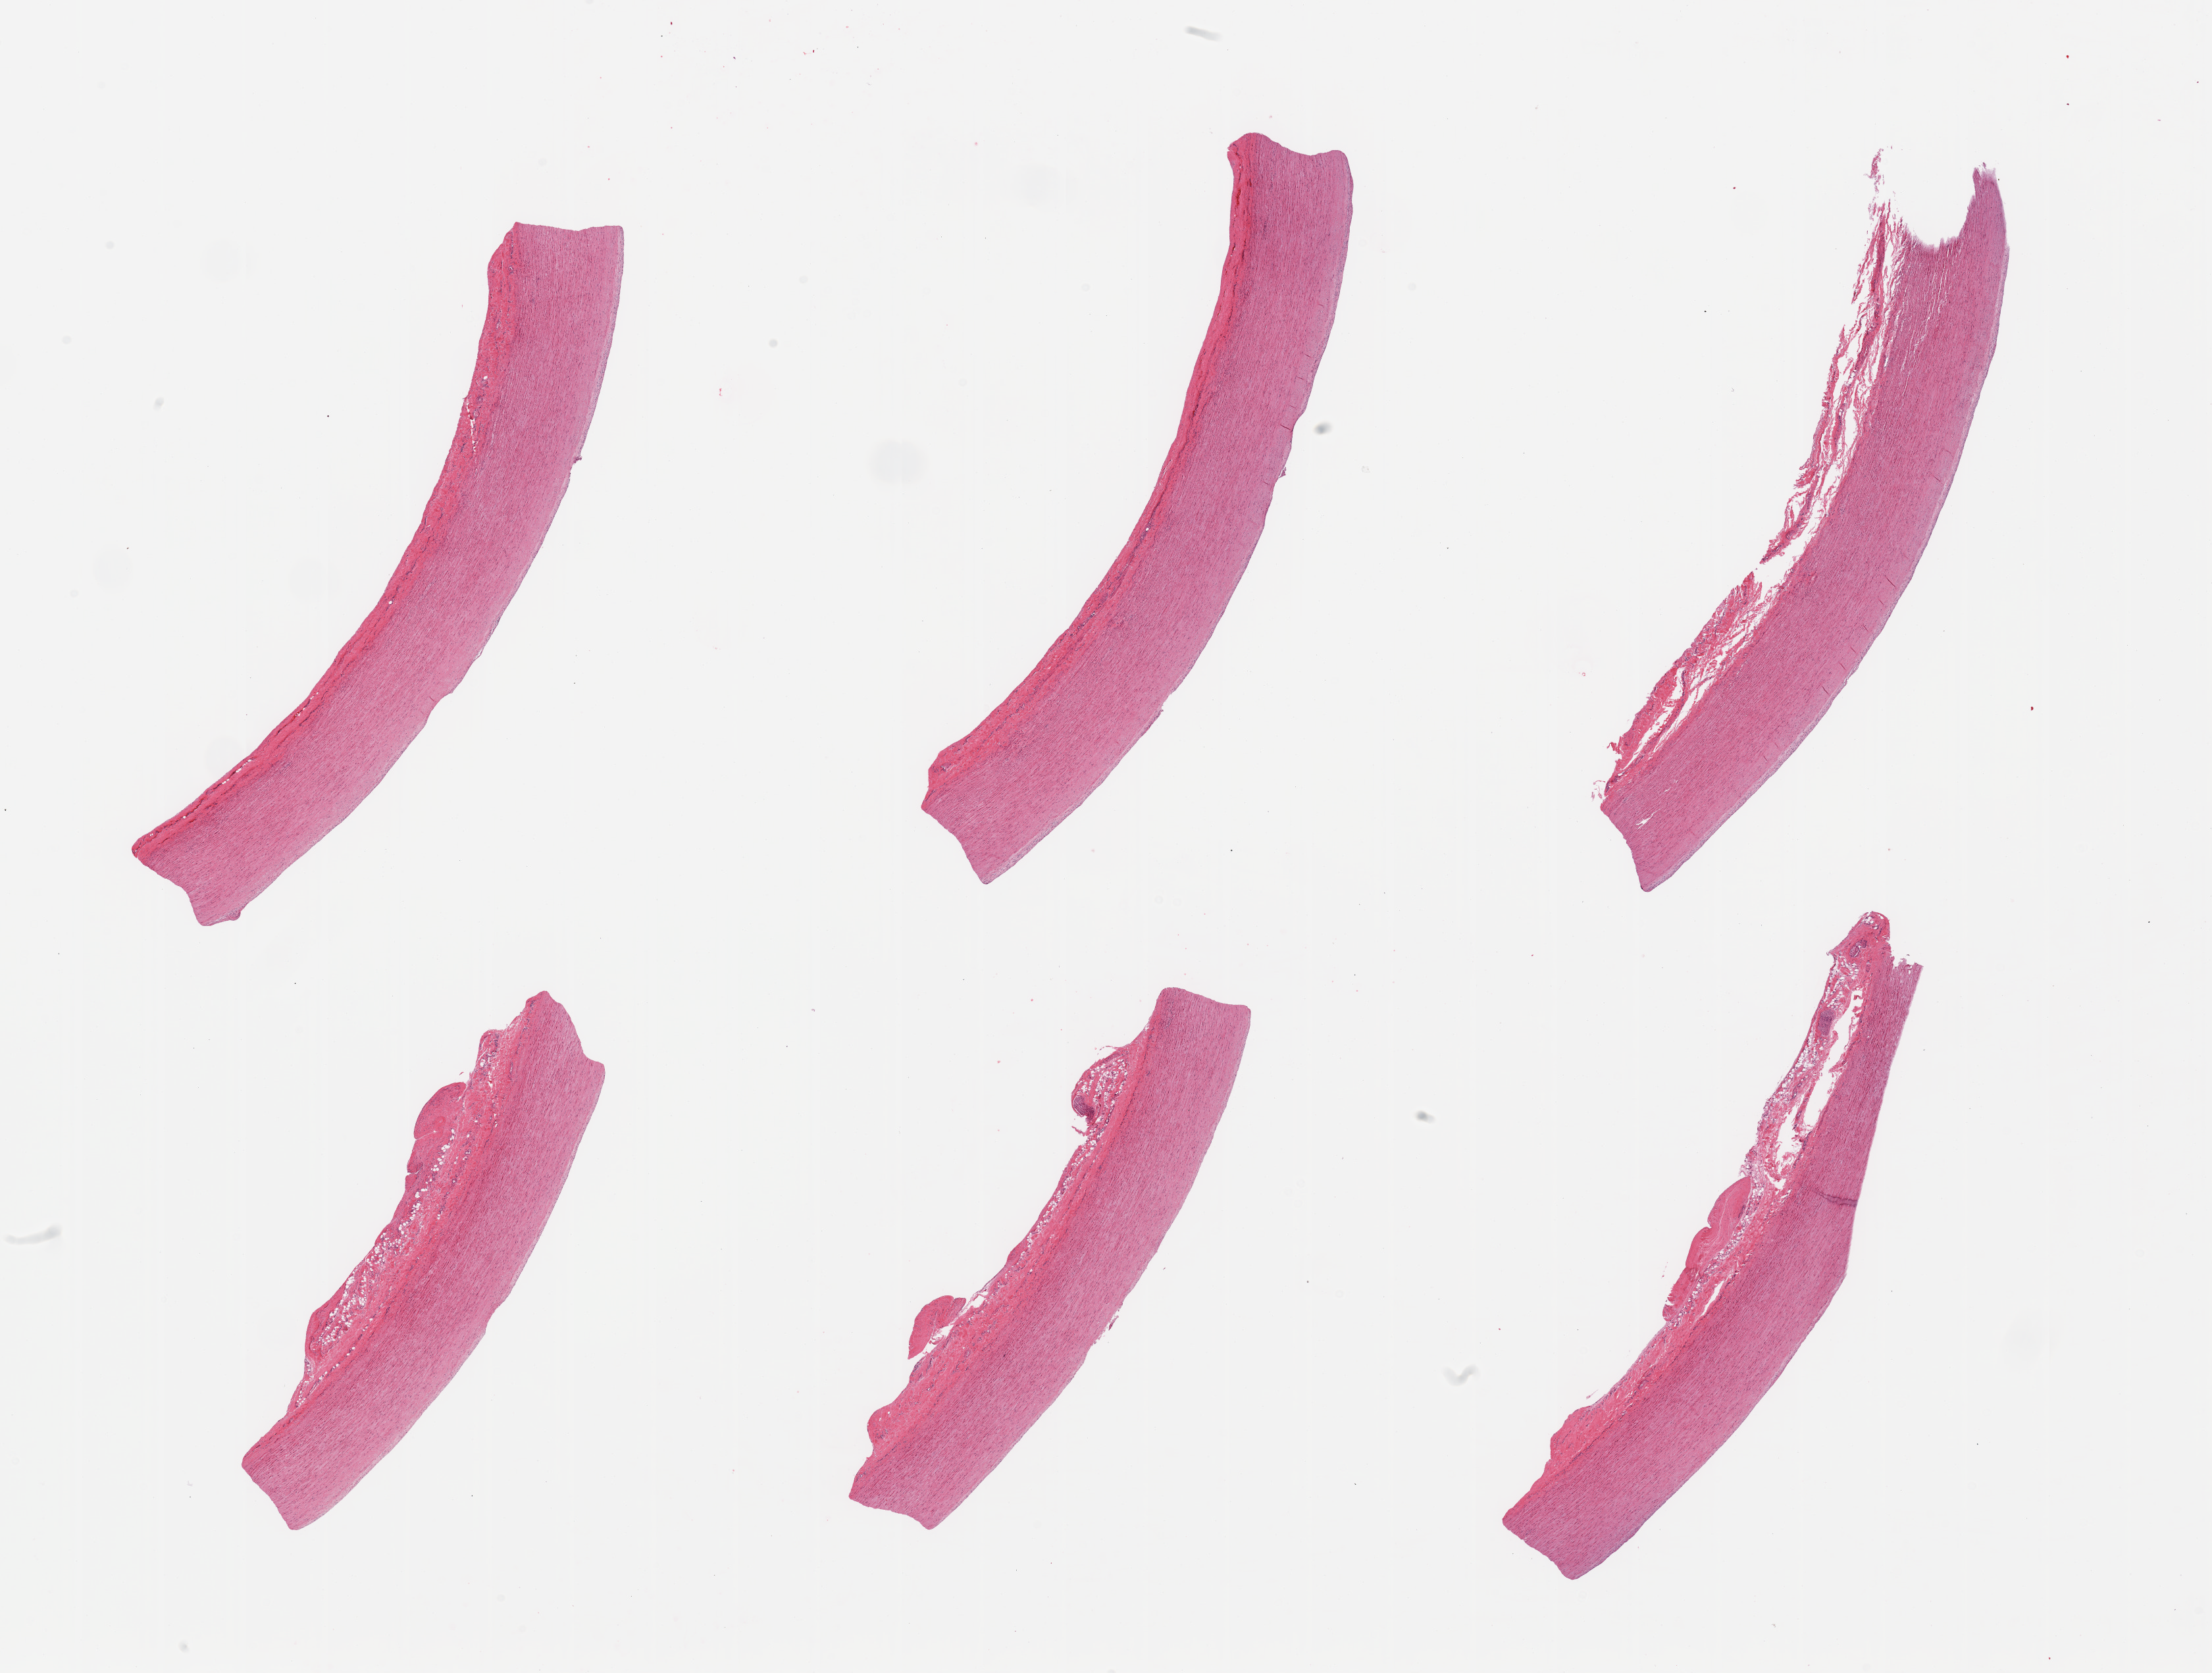
Digitized haematoxylin and eosin-stained section — a low-resolution overview of the entire scanned area, about 26.6 x 20.1 mm; PAXgene-fixed paraffin-embedded (PFPE) section; section of aorta (target tissue); donor tissue sample. Donor sex: male.
Pathologist's review note for this sample: 6 pieces, minimal atherosis.